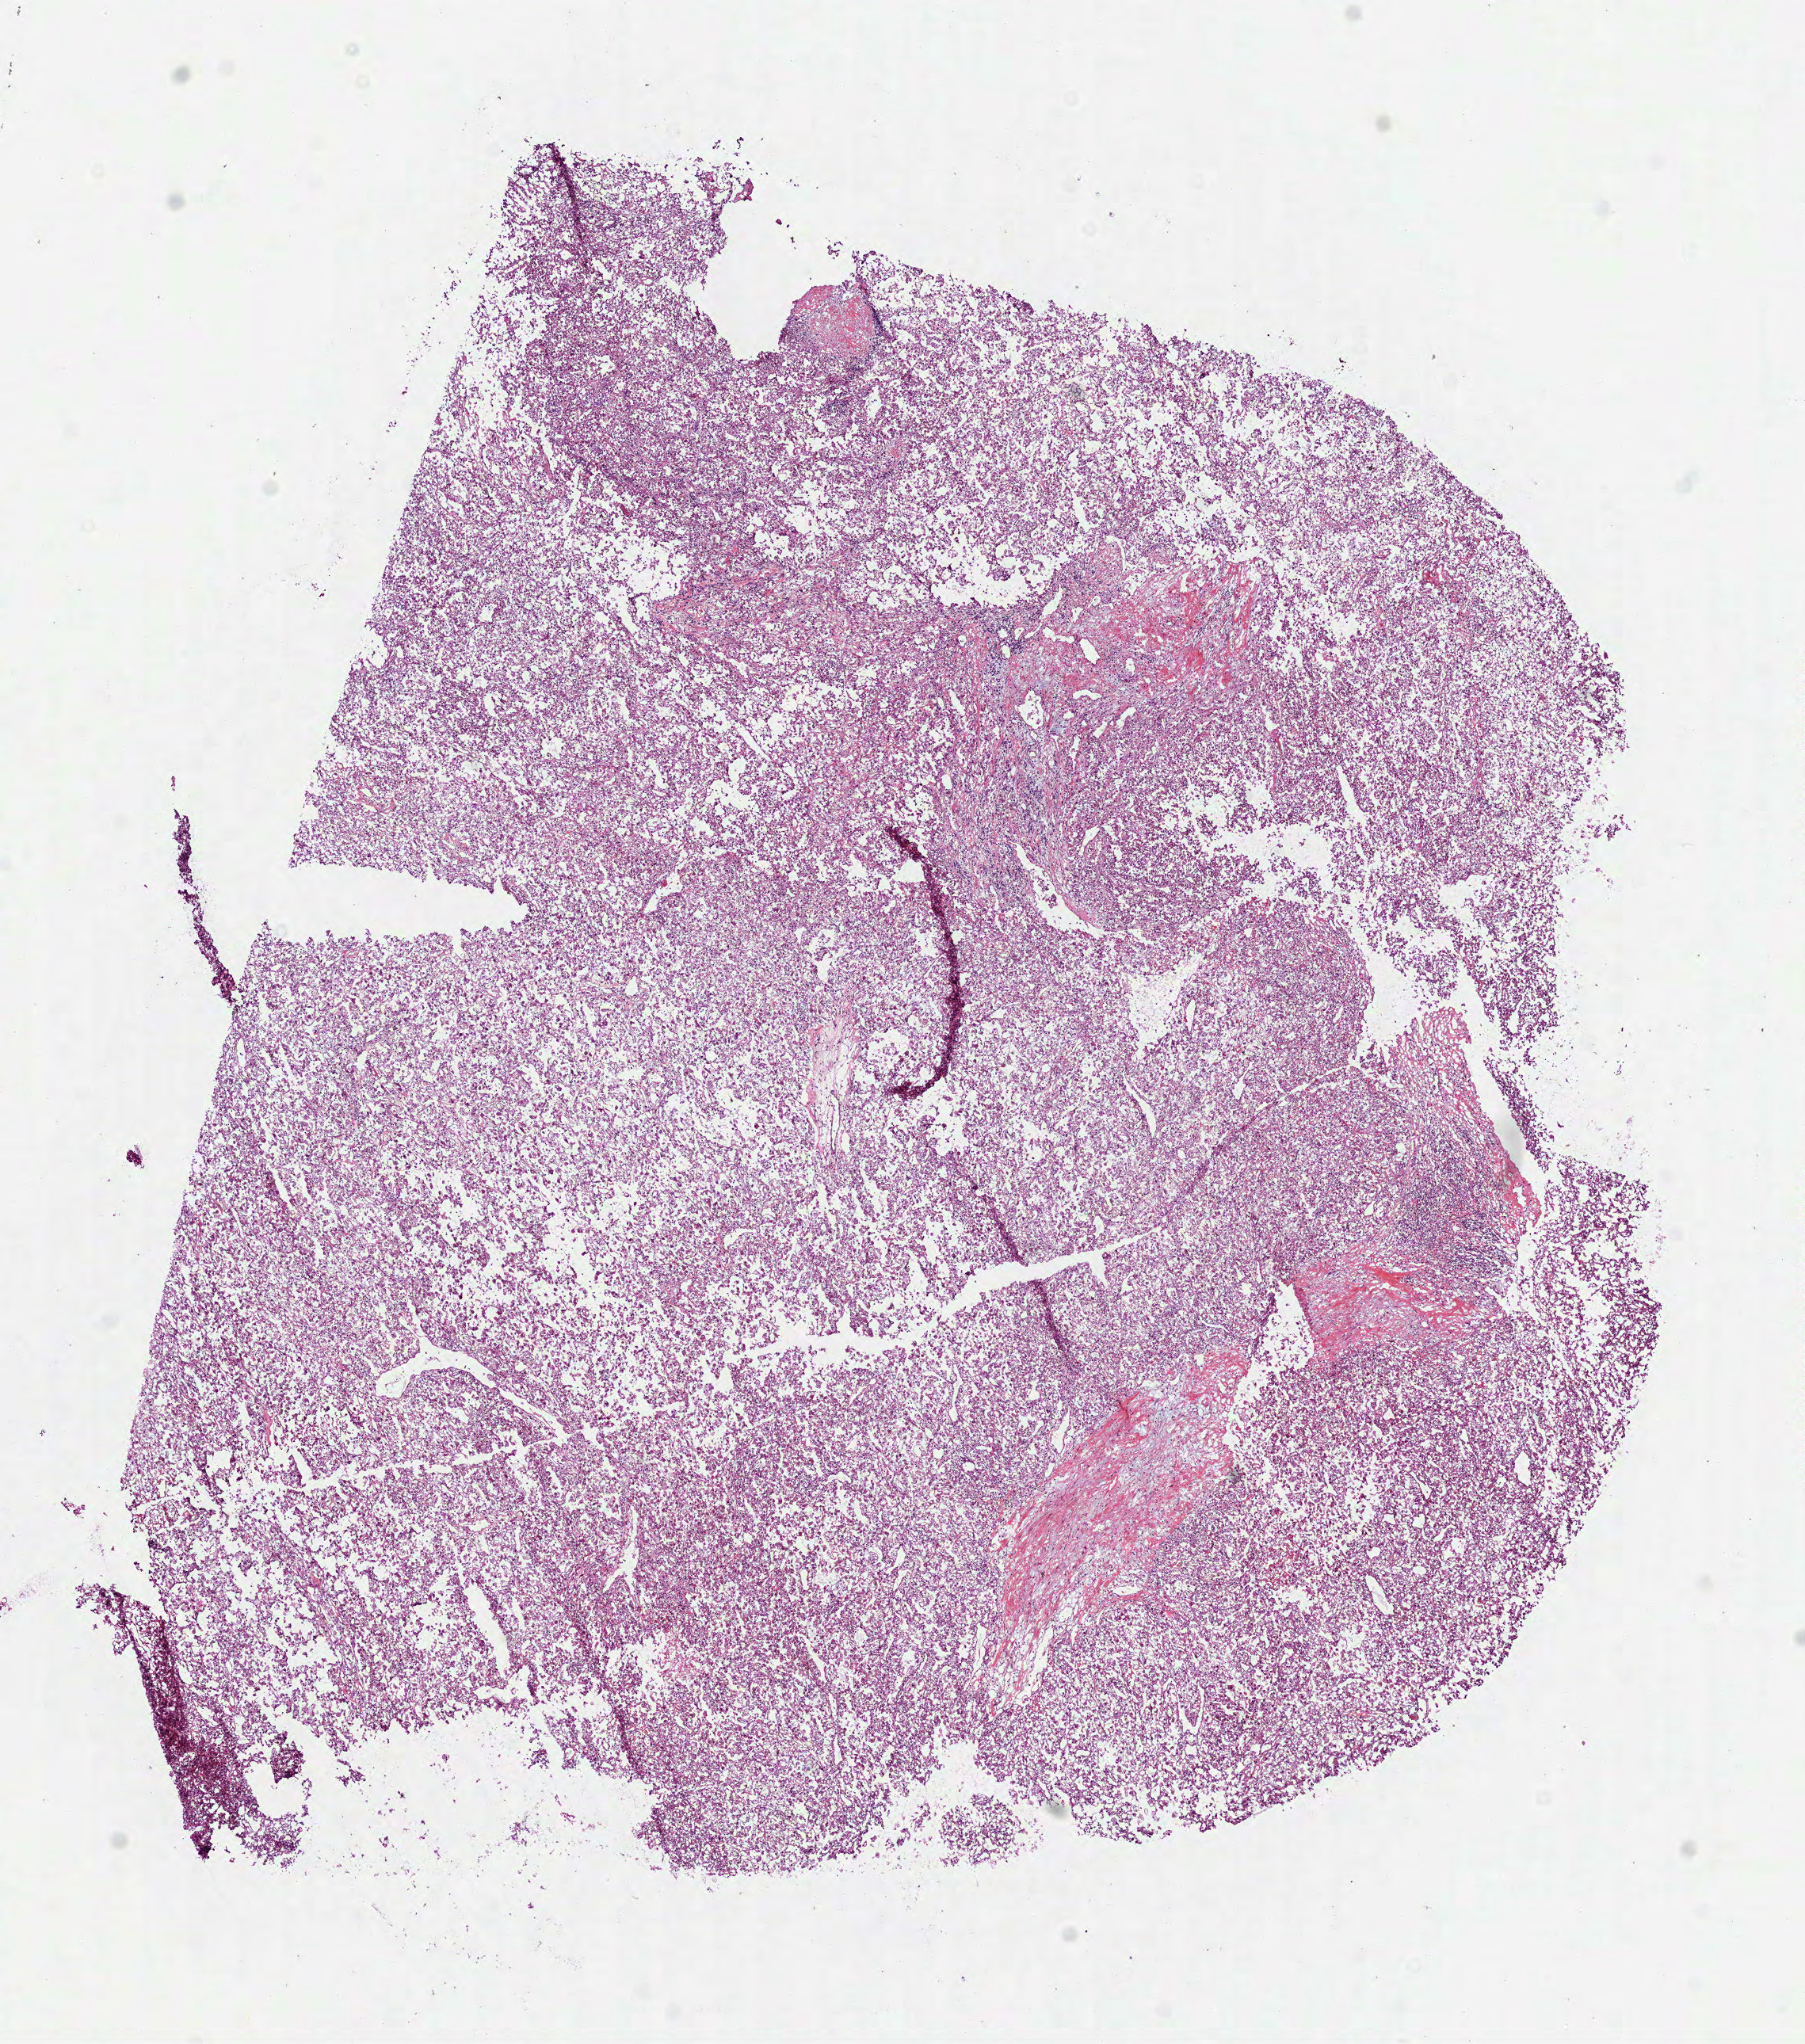
Whole-slide histology image, Hematoxylin and eosin (H&E) stained, a low-resolution overview of the entire scanned area, about 9.2 x 10.4 mm (from a 40x scan); frozen section from the bottom of the tissue portion; kidney, primary tumour sample. Male patient; age at initial diagnosis 77 years. Histologic grade: G4 (undifferentiated). Pathologist review of this section (percent, as recorded): tumour cells 85%, tumour nuclei 80%, normal cells 0%, stromal cells 15%, necrosis 0%.
• AJCC pathologic stage: I (6th edition)
• laterality: right
• pathologic diagnosis: Clear cell adenocarcinoma, NOS